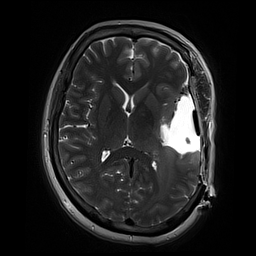
Brain MRI from a brain-tumour surgery series, one axial slice; slice 38 of 70 in the series (ordered by position); 2 mm slice thickness; 256 × 256 image matrix, field of view 220 × 220 mm. From the clinical record (not read from this slice): histopathology: Glioblastoma; WHO grade: 4; IDH mutation: no; tumour location: Left Temporal.
Outlined on this slice (expert manual segmentation):
- residual tumour: box from (x=154, y=107) to (x=174, y=141) px